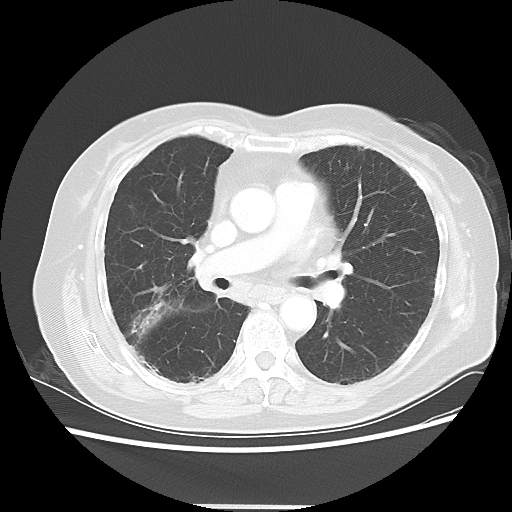
Chest CT, one axial slice. Position 26 of 50 along the scan axis. Reconstruction kernel LUNG. Lung window (W 1500 / L -600 HU). 5 mm slice thickness. 512 × 512 image matrix. Patient: female, 72 years. Case-level facts recorded for this patient, not image findings: clinical TNM (as recorded): T2 N1 M0.
Structures marked on this image (bounding box drawn by a radiologist):
- lung tumour (recorded histology: adenocarcinoma): bounding box (x1, y1, x2, y2) in pixels: (130, 300, 169, 338)